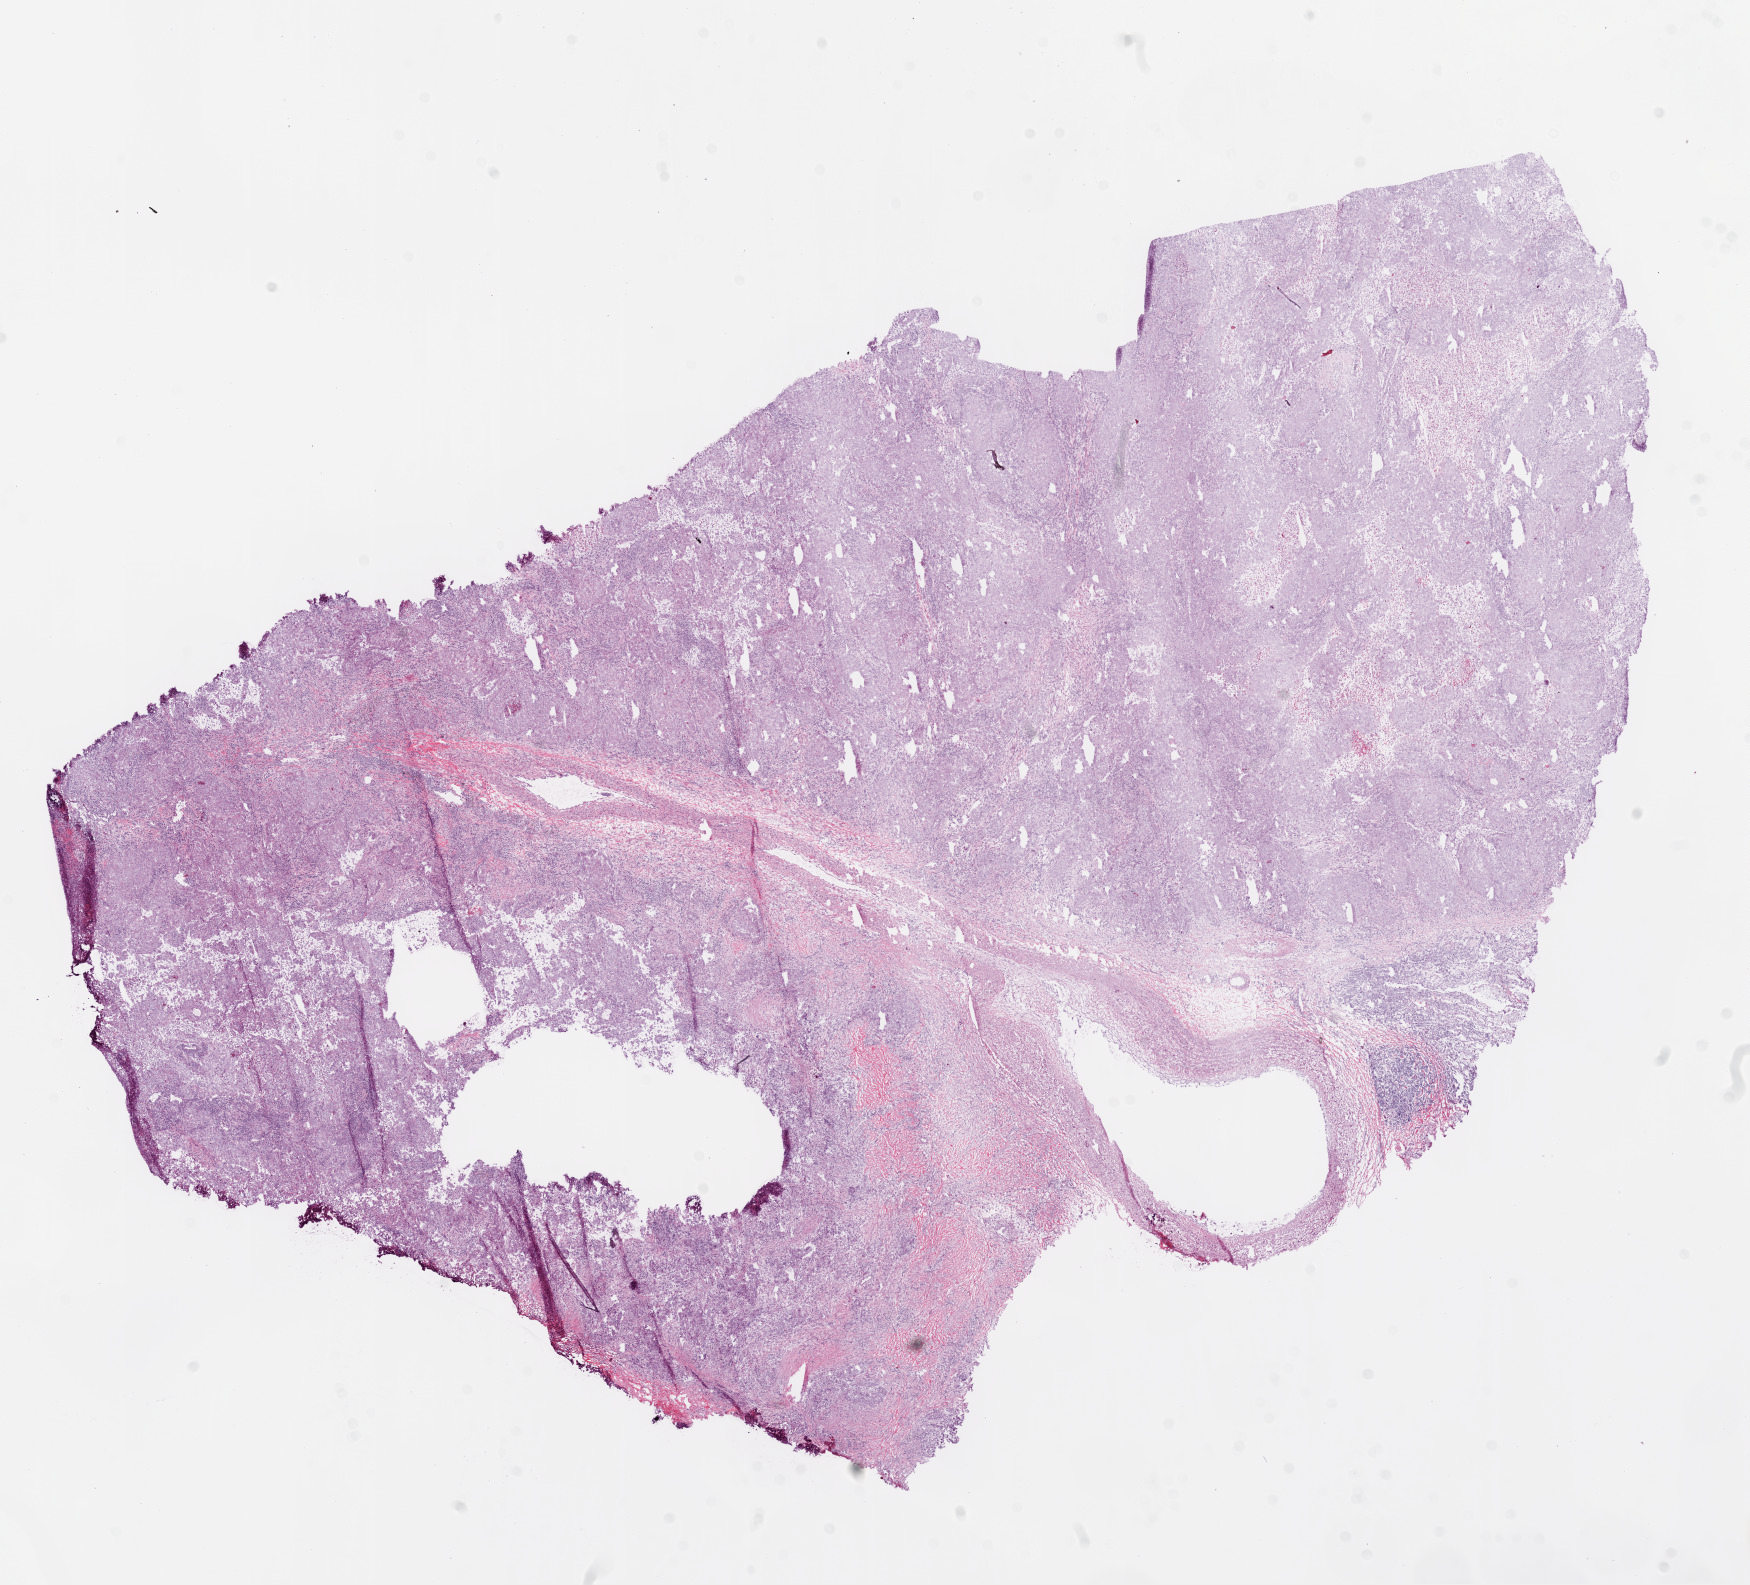
Digitized H&E tissue section (whole slide) — a low-resolution overview of the entire scanned area, about 14.0 x 12.7 mm (slide scanned at 20x); frozen section from the bottom of the tissue portion; primary tumour sample from the lung. Patient: female, age at initial diagnosis 47 years. Pathologist review of this section (percent, as recorded): tumour cells 92%, tumour nuclei 90%, normal cells 0%, stromal cells 5%, necrosis 3%.
Diagnosis: Squamous cell carcinoma, NOS (upper lobe, lung). AJCC pathologic stage: IIIA.